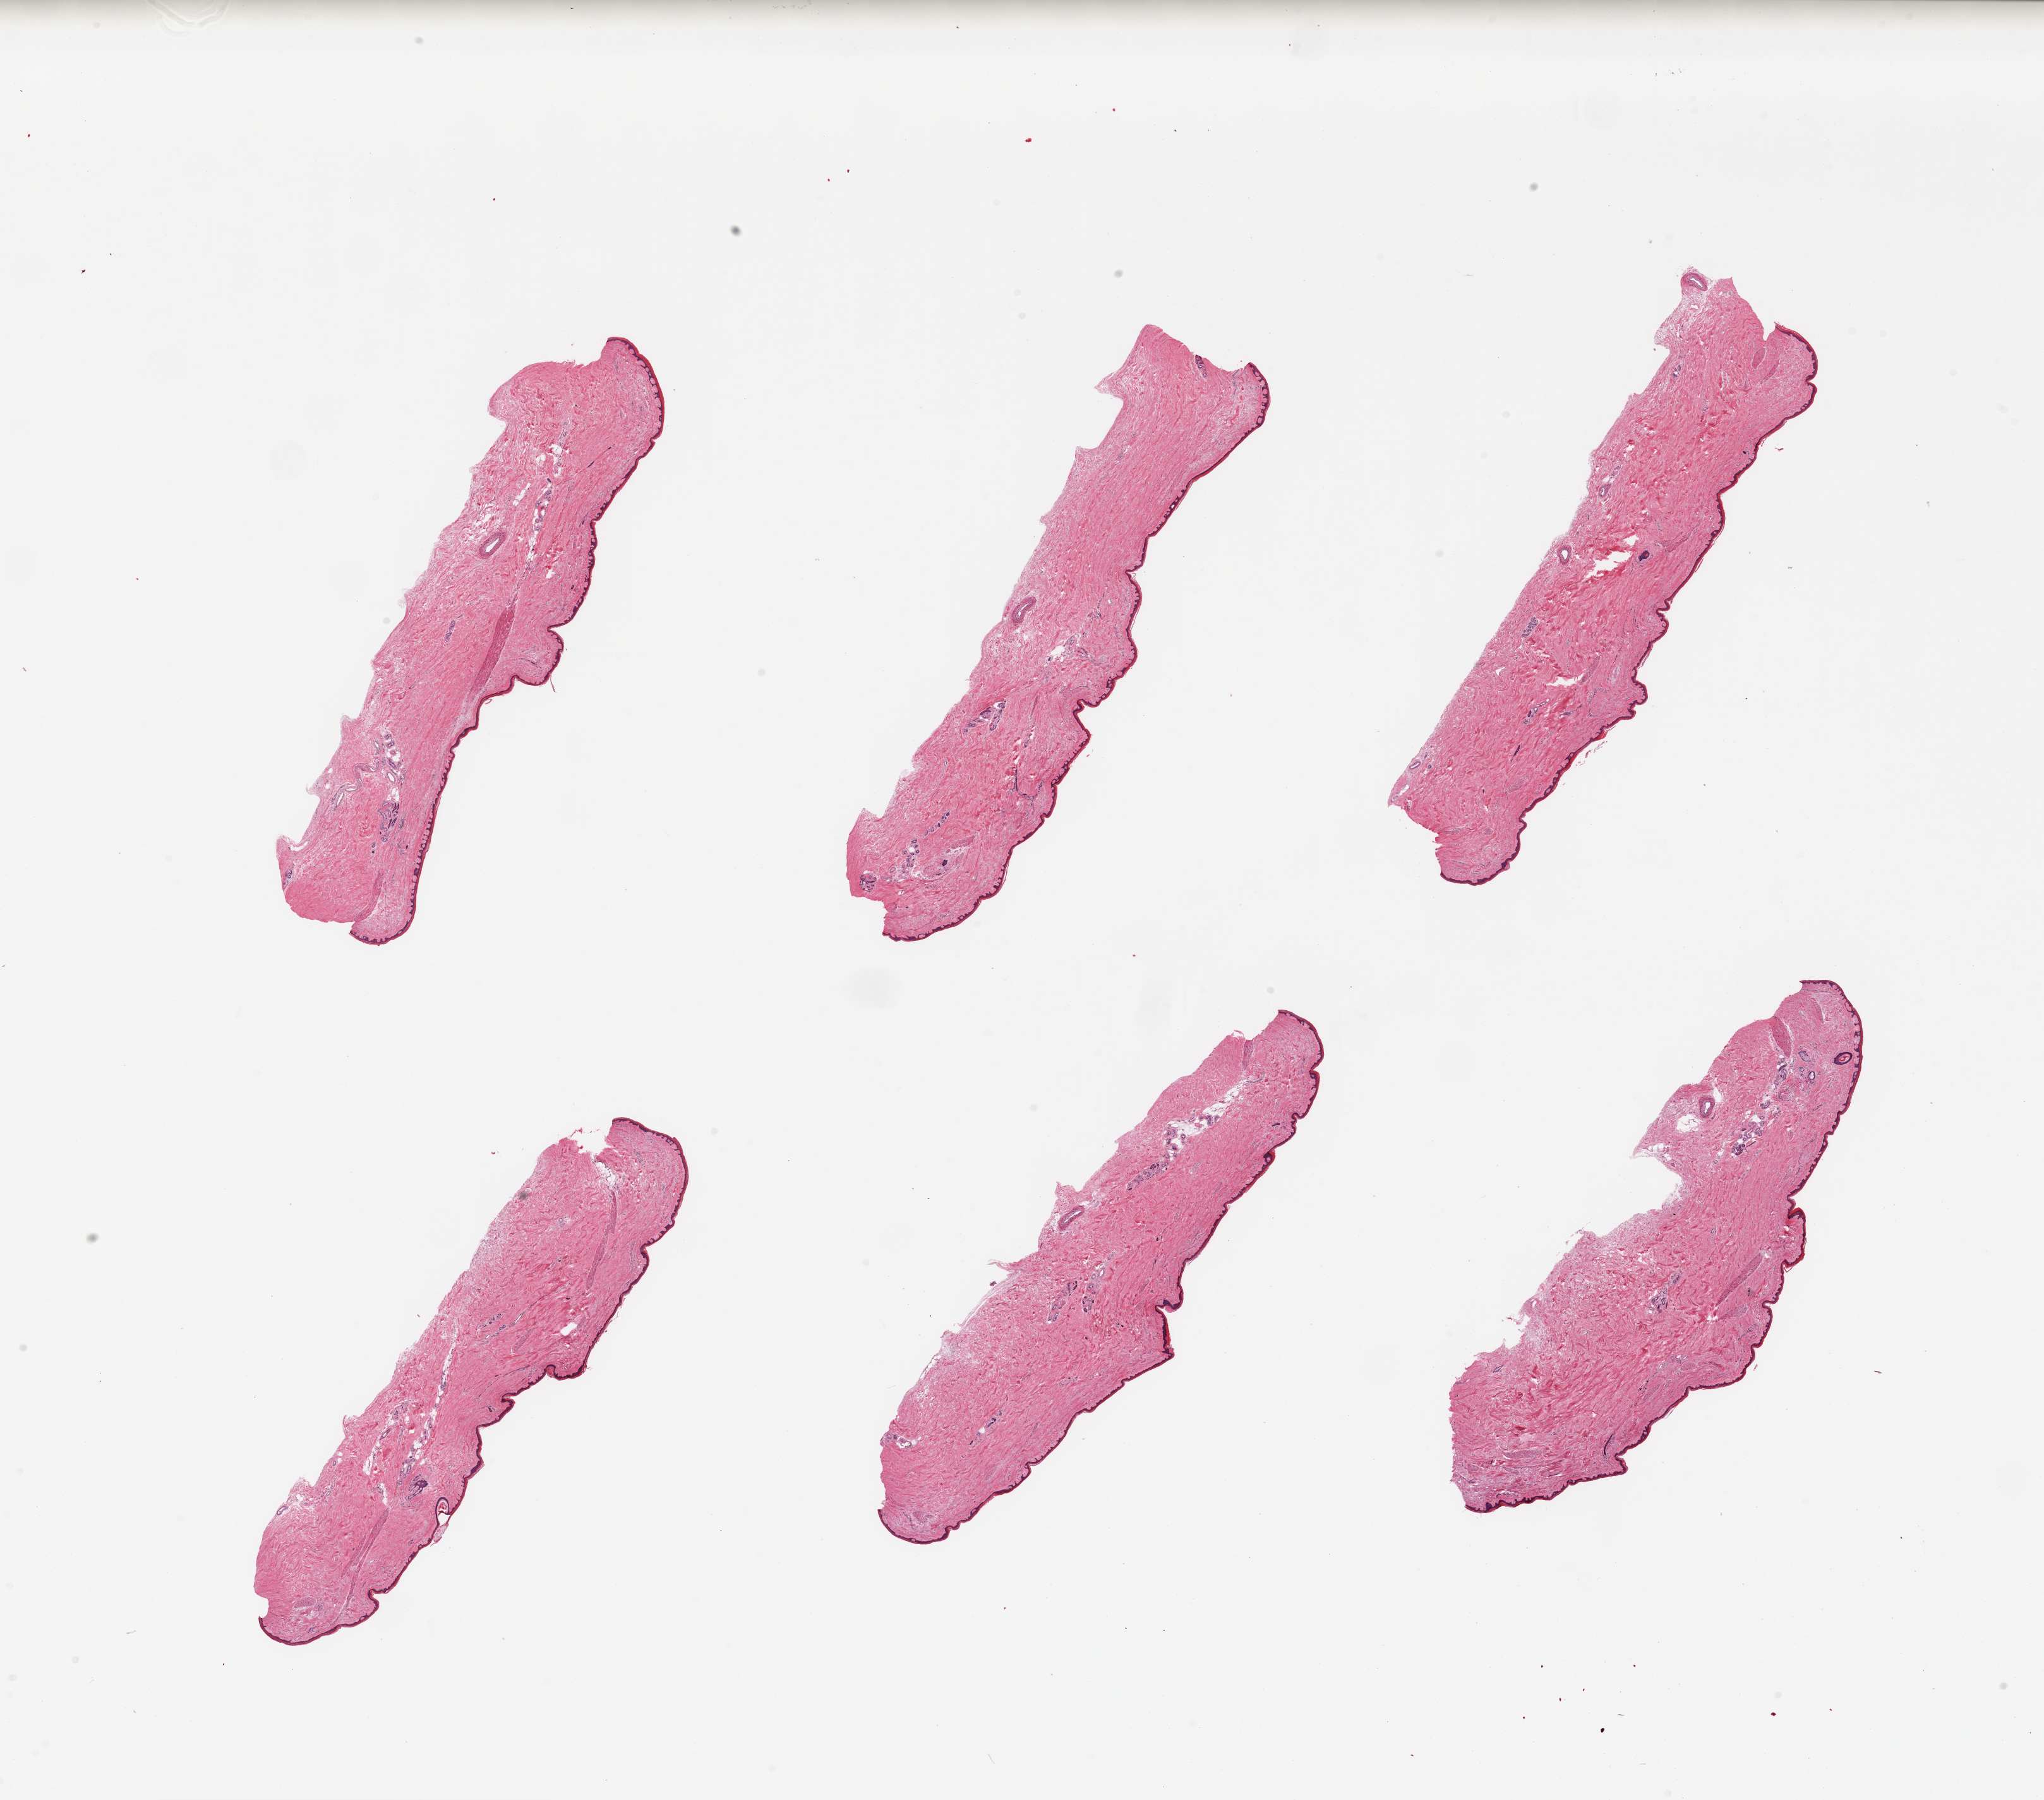
Haematoxylin and eosin whole-slide image — a low-resolution overview of the entire scanned area, about 25.6 x 22.5 mm; PAXgene-fixed paraffin-embedded (PFPE) section; target tissue: skin of lower leg; tissue donor sample. Male donor.
Pathologist's review note for this sample: 6 pieces; well trimmed; <5% dermal fat.